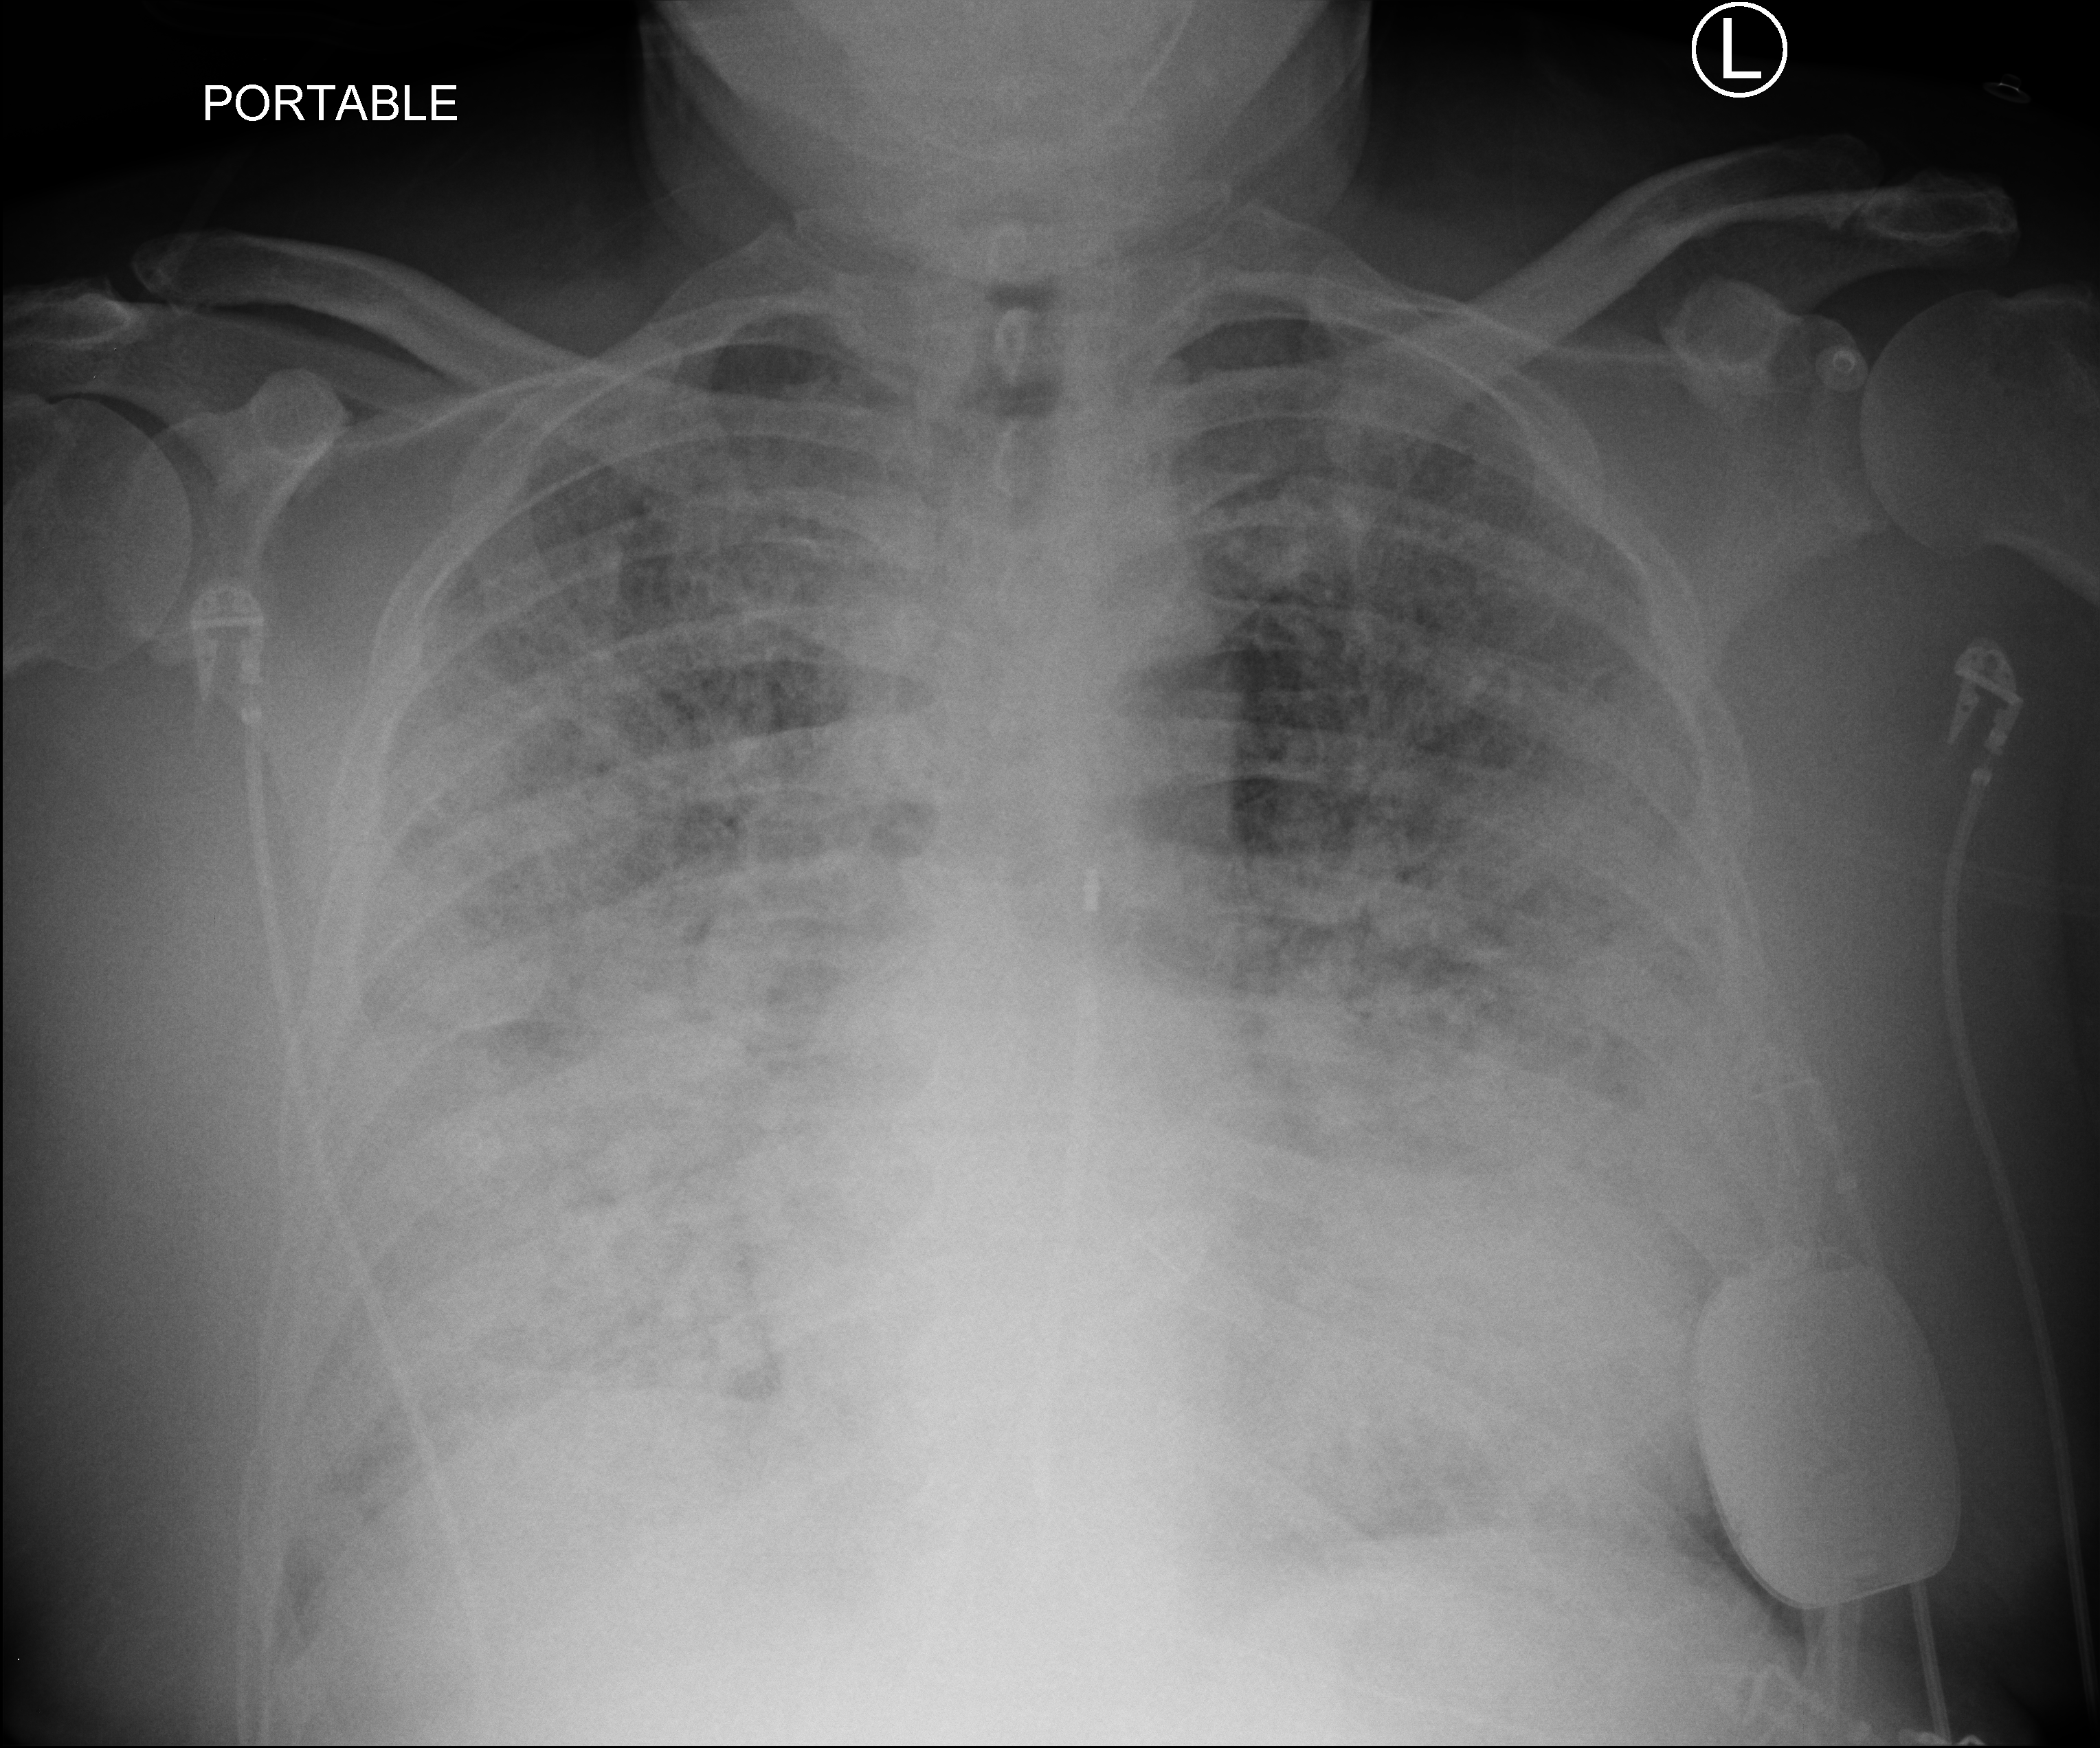
Portable chest radiograph, anteroposterior (AP) projection. Male patient hospitalised with COVID-19, age 60–74 years.
Admission-level facts for this patient (not findings on this image; timing relative to this image not recorded): admitted to intensive care during this hospital stay: yes.